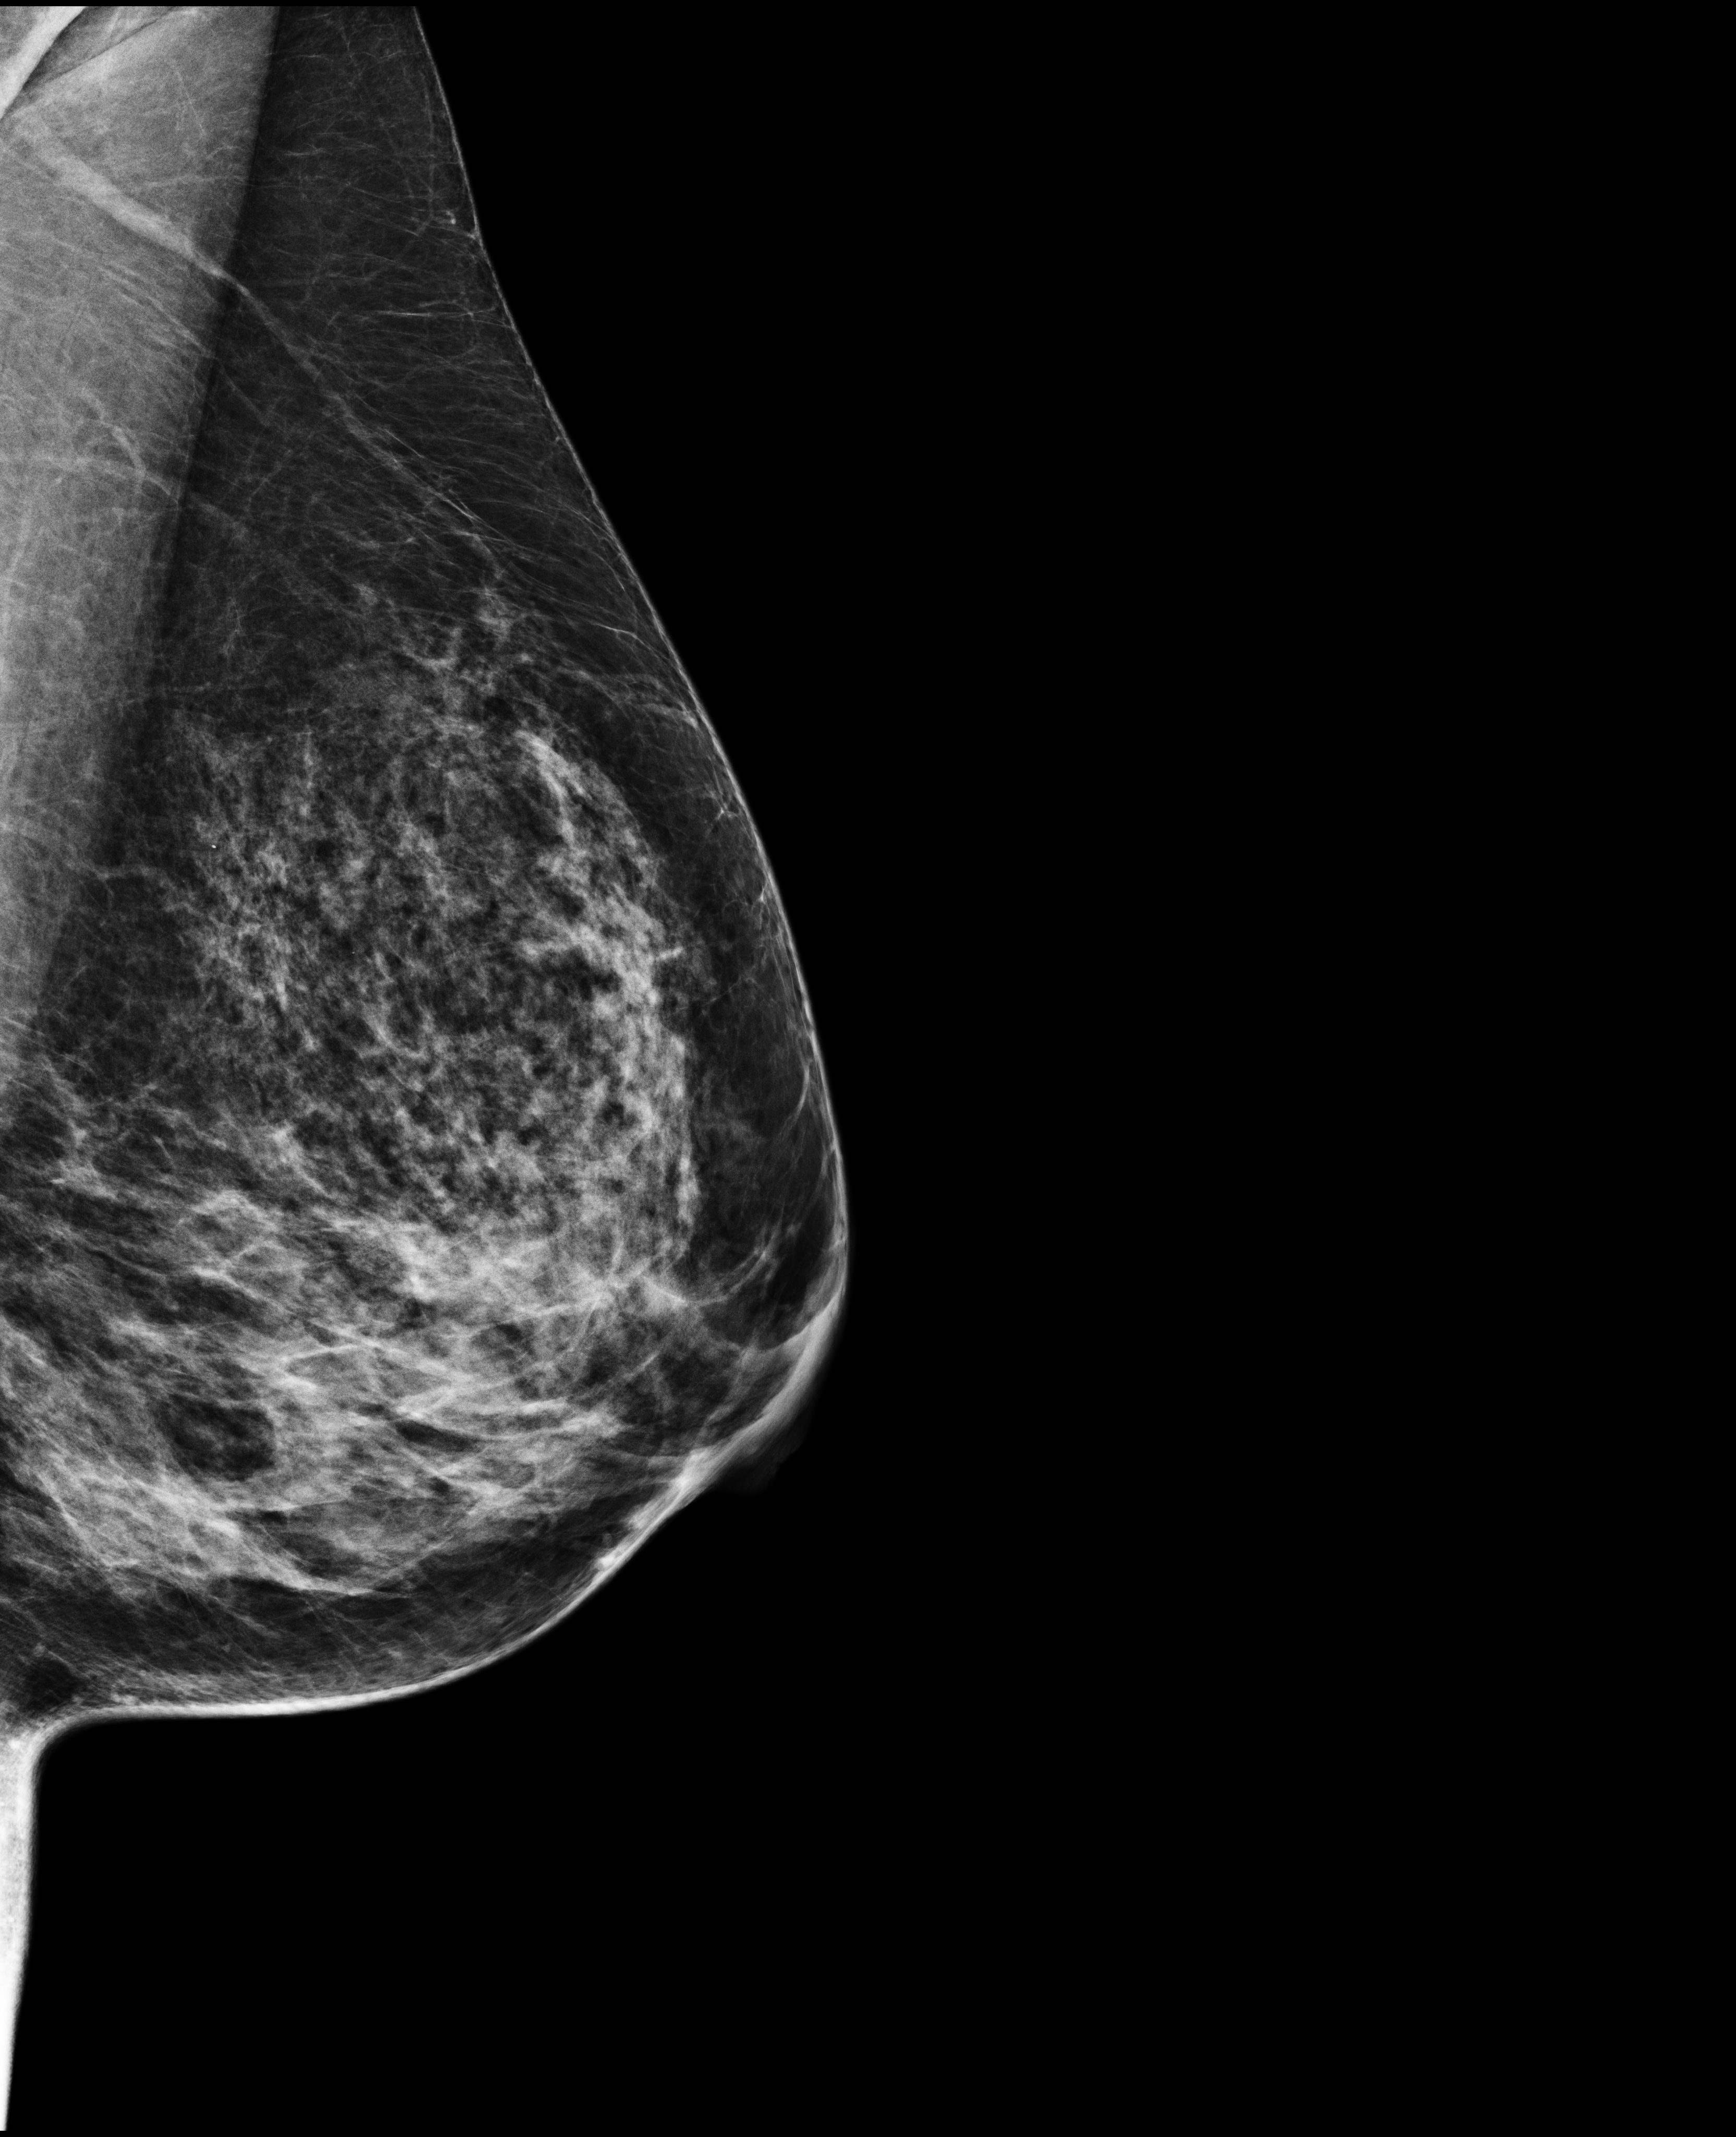
Annual screening mammography examination. Female patient, age 47 years.
Image type: full-field digital mammogram. Breast: left. Projection: mediolateral oblique (MLO) view.